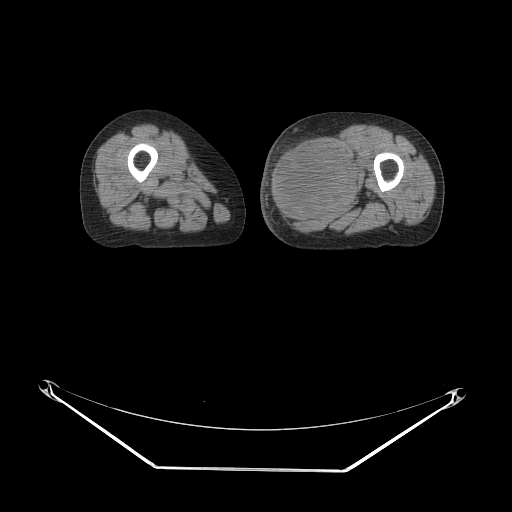
CT of an extremity soft-tissue mass (from a PET/CT study), one axial slice. Position 26 of 91 along the scan axis. Reconstruction kernel STANDARD. 140 kVp. Soft-tissue window (W 400 / L 40 HU). 512 × 512 image matrix, field of view 500 × 500 mm. Female patient. Case-level facts recorded for this patient, not image findings: histological type: pleomorphic leiomyosarcoma; grade: high; site of the primary tumour: left thigh.
Outlined on this slice (expert contour drawn on MRI and transferred to this co-registered scan by the dataset authors):
- gross tumour volume including surrounding oedema: box from (x=270, y=135) to (x=357, y=220) px
- gross tumour volume (mass): (x=270, y=137)–(x=355, y=220)